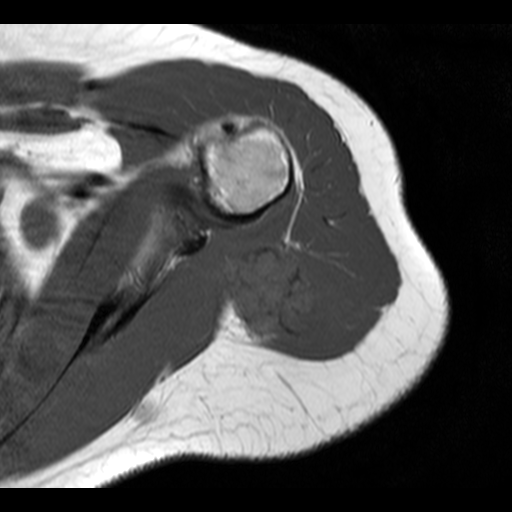
MRI of an extremity soft-tissue mass, one axial slice. Position 10 of 20 along the scan axis. 512 × 512 image matrix, field of view 150 × 150 mm. Female patient. Case-level facts recorded for this patient, not image findings: histological type: malignant fibrous histiocytoma; grade: low; site of the primary tumour: left arm.
Annotated regions visible in this slice (expert manual segmentation):
- gross tumour volume (mass): bounding box [x1, y1, x2, y2] px = [221, 247, 336, 349]